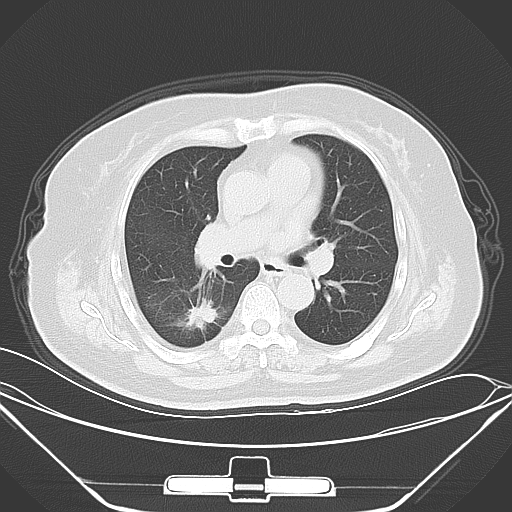
Chest CT, one axial slice; slice 36 of 64 in the series (ordered by position); lung window (W 1500 / L -600 HU); 5 mm slice thickness; 512 × 512 image matrix, field of view 396 × 396 mm. Patient: female, 70 years. From the clinical record (not read from this slice): clinical TNM (as recorded): T2 N0 M3.
Outlined on this slice (bounding box drawn by a radiologist):
- lung tumour (recorded histology: adenocarcinoma): bounding box (x1, y1, x2, y2) in pixels: (168, 293, 223, 344)